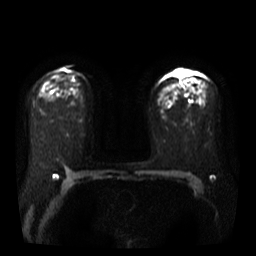
Breast MRI, one axial slice. Position 24 of 40 along the scan axis. Diffusion-weighted series; image 2 of 4 stored at this slice position (different b-values; order by instance number). 3 T. 256 × 256 image matrix, field of view 360 × 360 mm. Female patient.
Structures marked on this image (manually delineated by an expert):
- tumour on diffusion-weighted imaging: bounding box <177,71,188,77> (left, top, right, bottom; pixels)